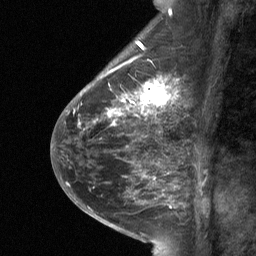
Breast MRI (dynamic contrast-enhanced), one sagittal slice; position 24 of 64 along the scan axis; dynamic contrast-enhanced study with each time point stored as its own series, time point 2 of 3 at this slice position (early post-contrast, ordered by acquisition time); 1.5 T; TE 4.8 ms, TR 27 ms; 256 × 256 image matrix, field of view 180 × 180 mm. Patient: female, 59 years. Case-level facts recorded for this patient, not image findings: setting: breast cancer imaged before/during neoadjuvant chemotherapy; receptor status: triple-negative.
Annotated regions visible in this slice (semi-automatically segmented with operator editing):
- analysis volume of interest (the breast-tissue region the enhancement analysis was run in; not a lesion): bounding box (x1, y1, x2, y2) in pixels: (113, 66, 175, 120)
- tumour enhancement mask (voxels above the 90 % enhancement threshold inside the analysis volume of interest): (113, 69, 175, 119)